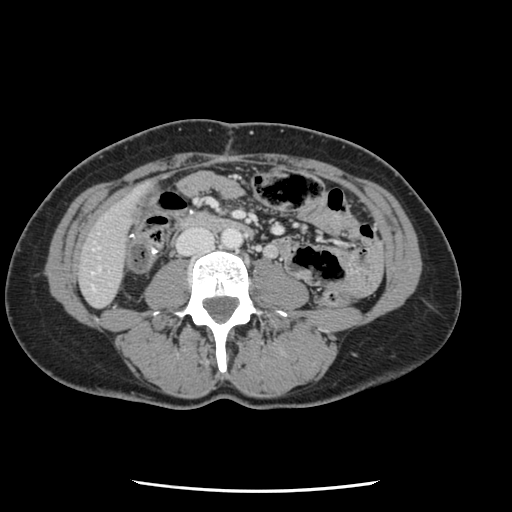
Contrast-enhanced abdominal CT, one axial slice. Slice 13 of 134 in the series (ordered by position). 120 kVp. Intravenous contrast given. Soft-tissue window (W 400 / L 40 HU). 2.5 mm slice thickness. 512 × 512 image matrix, field of view 330 × 330 mm. Female patient, age 43 years. Case-level facts recorded for this patient, not image findings: diagnosis: colorectal cancer liver metastases, imaged before liver resection.
Structures marked on this image (outlined manually by an expert reader):
- liver: bounding box (x1, y1, x2, y2) in pixels: (80, 193, 139, 307)
- planned liver remnant (the part of the liver to remain after resection): (80, 193, 138, 307)